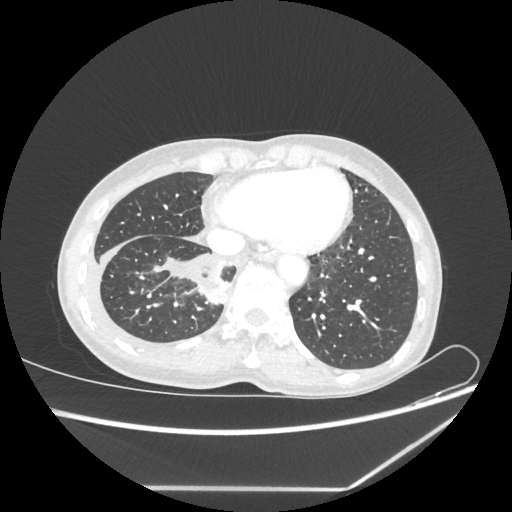
Chest CT, one axial slice. Position 62 of 237 along the scan axis. Reconstruction kernel STANDARD. Lung window (W 1500 / L -600 HU). 1.25 mm slice thickness. 512 × 512 image matrix, field of view 364 × 364 mm. Female patient, age 59 years. From the clinical record (not read from this slice): clinical TNM (as recorded): T1c N1 M1.
Outlined on this slice (bounding box drawn by a radiologist):
- lung tumour (recorded histology: adenocarcinoma): bounding box <198,283,229,307> (left, top, right, bottom; pixels)